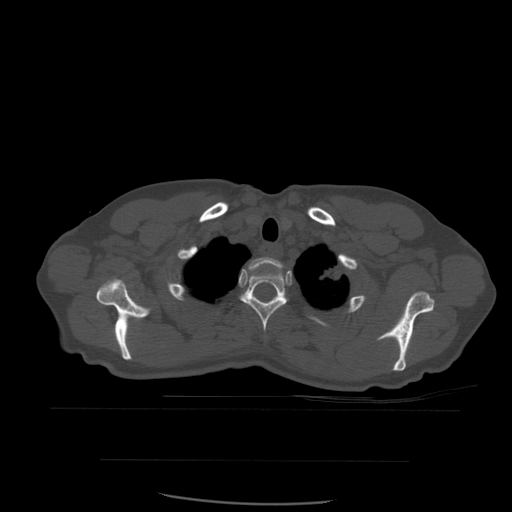
CT including the spine, one axial slice; bone window (W 1800 / L 400 HU); 1.25 mm slice thickness; 512 × 512 image matrix. Patient age 48 years. From the clinical record (not read from this slice): primary cancer: lung.
Annotated regions visible in this slice (semi-automatically segmented with operator editing):
- T1 vertebra: bounding box [x1, y1, x2, y2] px = [249, 257, 283, 270]
- T2 vertebra: [240, 264, 288, 333]
- T3 vertebra: [257, 299, 270, 303]